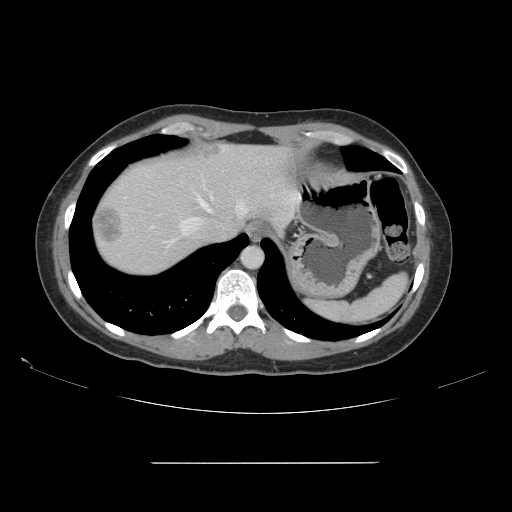
Contrast-enhanced abdominal CT, one axial slice. Position 131 of 151 along the scan axis. 120 kVp. Intravenous contrast given. Soft-tissue window (W 400 / L 40 HU). 2.5 mm slice thickness. 512 × 512 image matrix. Female patient, age 46 years. From the clinical record (not read from this slice): diagnosis: colorectal cancer liver metastases, imaged before liver resection; multiple liver metastases: yes; largest metastasis: 3 cm; disease in both lobes: yes.
Annotated regions visible in this slice (outlined manually by an expert reader):
- hepatic veins: box from (x=181, y=196) to (x=248, y=235) px
- liver: (x=92, y=144)–(x=289, y=276)
- planned liver remnant (the part of the liver to remain after resection): (x=105, y=147)–(x=291, y=239)
- liver metastasis: (x=96, y=205)–(x=123, y=247)
- liver metastasis: (x=197, y=147)–(x=220, y=159)